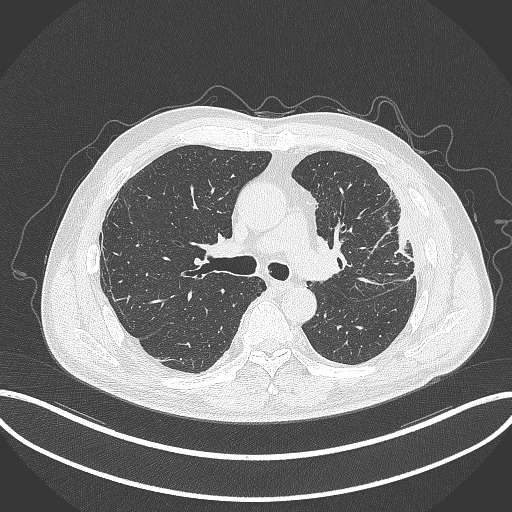
Chest CT, one axial slice; lung window (W 1500 / L -600 HU); 1 mm slice thickness; 512 × 512 image matrix, field of view 415 × 415 mm. Patient: male, 64 years. From the clinical record (not read from this slice): clinical TNM (as recorded): T4 N1 M0; histopathological grade: G3.
Outlined on this slice (rectangle marked by the reading radiologist):
- lung tumour (recorded histology: adenocarcinoma): bounding box (x1, y1, x2, y2) in pixels: (389, 208, 415, 263)